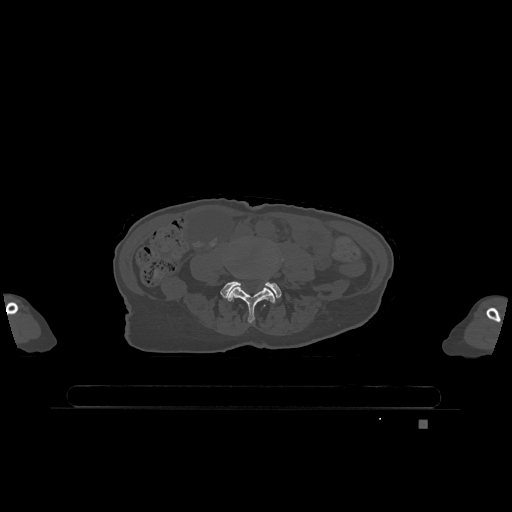
CT including the spine, one axial slice; bone window (W 1800 / L 400 HU); 512 × 512 image matrix. Female patient, age 74 years. From the clinical record (not read from this slice): primary cancer: lung; vertebrae with lytic lesions (as recorded): T1, T4, T5, T6, L4, L5.
Outlined on this slice (semi-automatically segmented with operator editing):
- L4 vertebra: bounding box (x1, y1, x2, y2) in pixels: (228, 256, 283, 323)
- L5 vertebra: (220, 281, 282, 301)